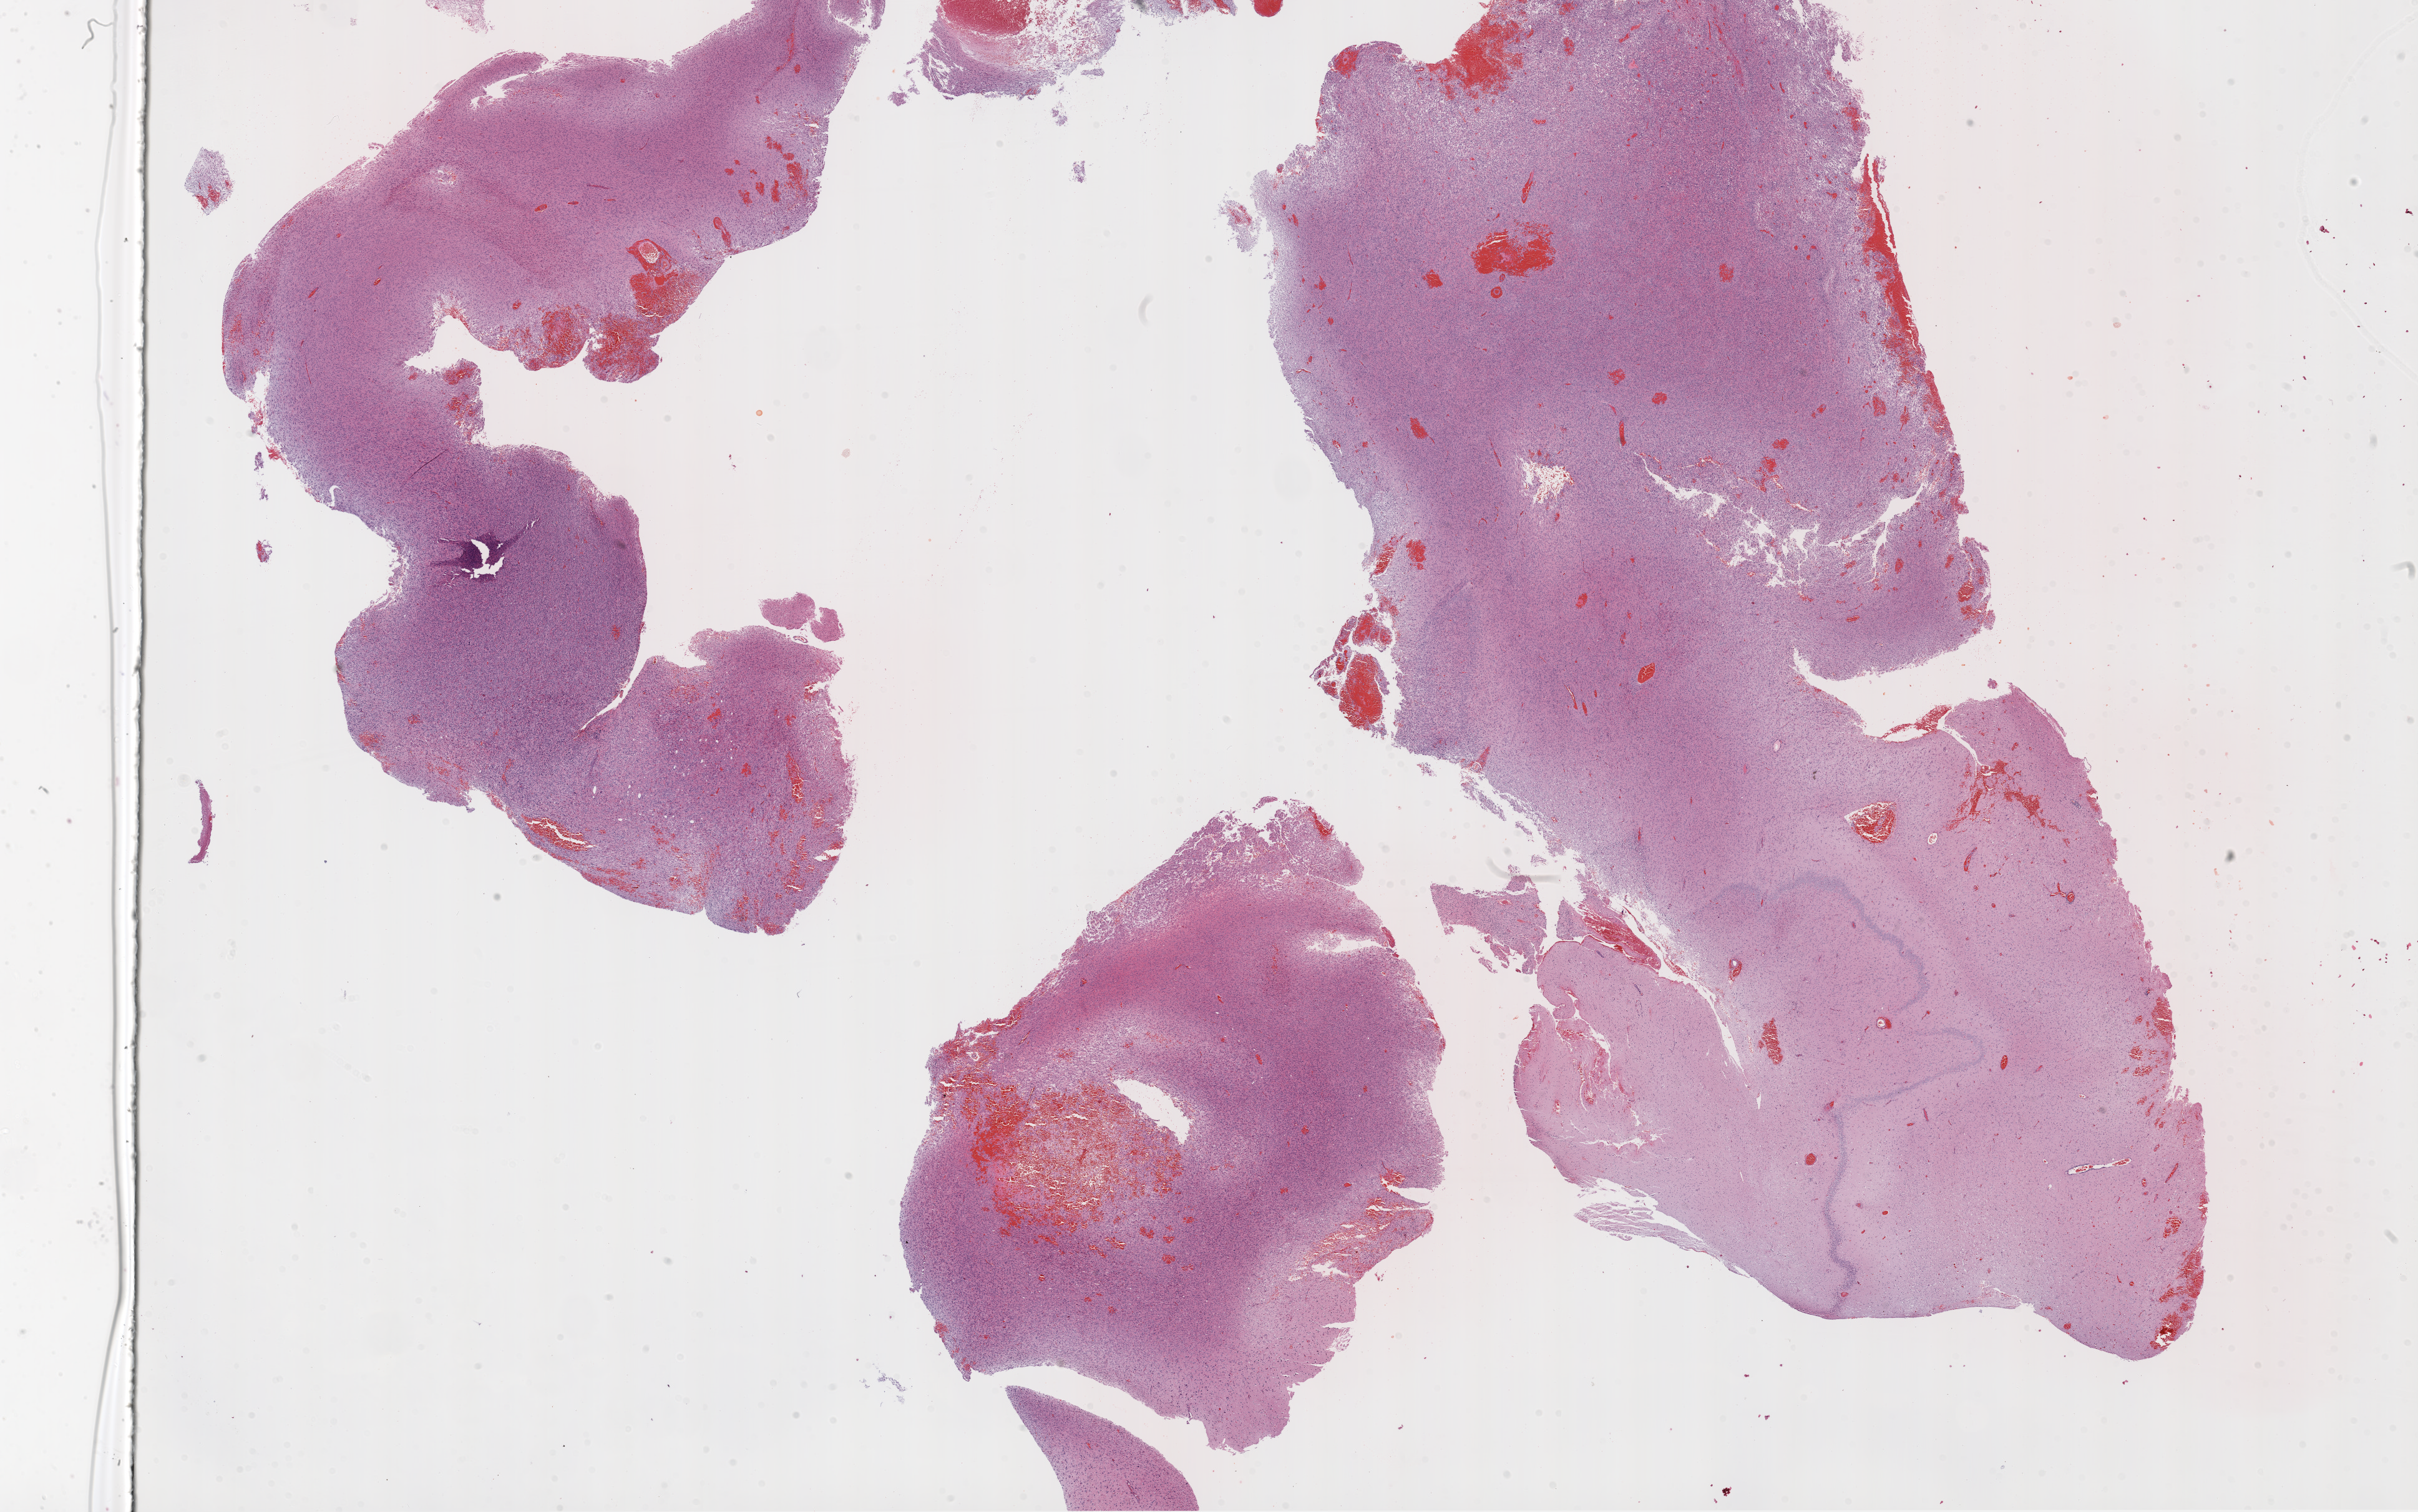
H&E-stained whole-slide image — low-resolution overview of the scanned area, about 31.1 x 19.4 mm, formalin-fixed paraffin-embedded (FFPE) diagnostic section, brain, primary tumour sample. Male patient; age at initial diagnosis 60 years.
Histologic diagnosis: Glioblastoma.